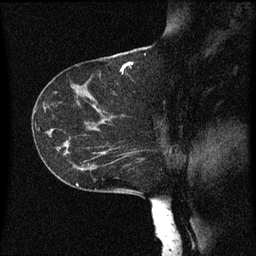
Breast MRI (dynamic contrast-enhanced), one sagittal slice. Position 36 of 60 along the scan axis. Dynamic contrast-enhanced series, image 2 of 3 at this slice position (ordered by acquisition). 1.5 T. TE 4.2 ms, TR 8 ms. 2 mm slice thickness. 256 × 256 image matrix, field of view 200 × 200 mm. Patient: female, 55 years.
Structures marked on this image (semi-automatic segmentation, software-assisted and operator-edited):
- analysis volume of interest (the breast-tissue region the enhancement analysis was run in; not a lesion): bounding box <46,124,149,183> (left, top, right, bottom; pixels)
- tumour enhancement mask (voxels above the 70 % enhancement threshold inside the analysis volume of interest): <98,148,143,161>